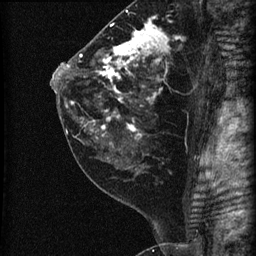
Breast MRI (dynamic contrast-enhanced), one sagittal slice; slice 36 of 60 in the series (ordered by position); dynamic contrast-enhanced series, image 2 of 3 at this slice position (ordered by acquisition); 1.5 T; TE 4.2 ms, TR 22.7 ms; 1.8 mm slice thickness; 256 × 256 image matrix, field of view 180 × 180 mm. Patient: female, 45 years. From the clinical record (not read from this slice): setting: breast cancer imaged before/during neoadjuvant chemotherapy; receptor status: HR-positive, HER2-negative.
Outlined on this slice (semi-automatic segmentation, software-assisted and operator-edited):
- analysis volume of interest (the breast-tissue region the enhancement analysis was run in; not a lesion): box from (x=74, y=11) to (x=205, y=140) px
- tumour enhancement mask (voxels above the 90 % enhancement threshold inside the analysis volume of interest): (x=79, y=17)–(x=168, y=138)